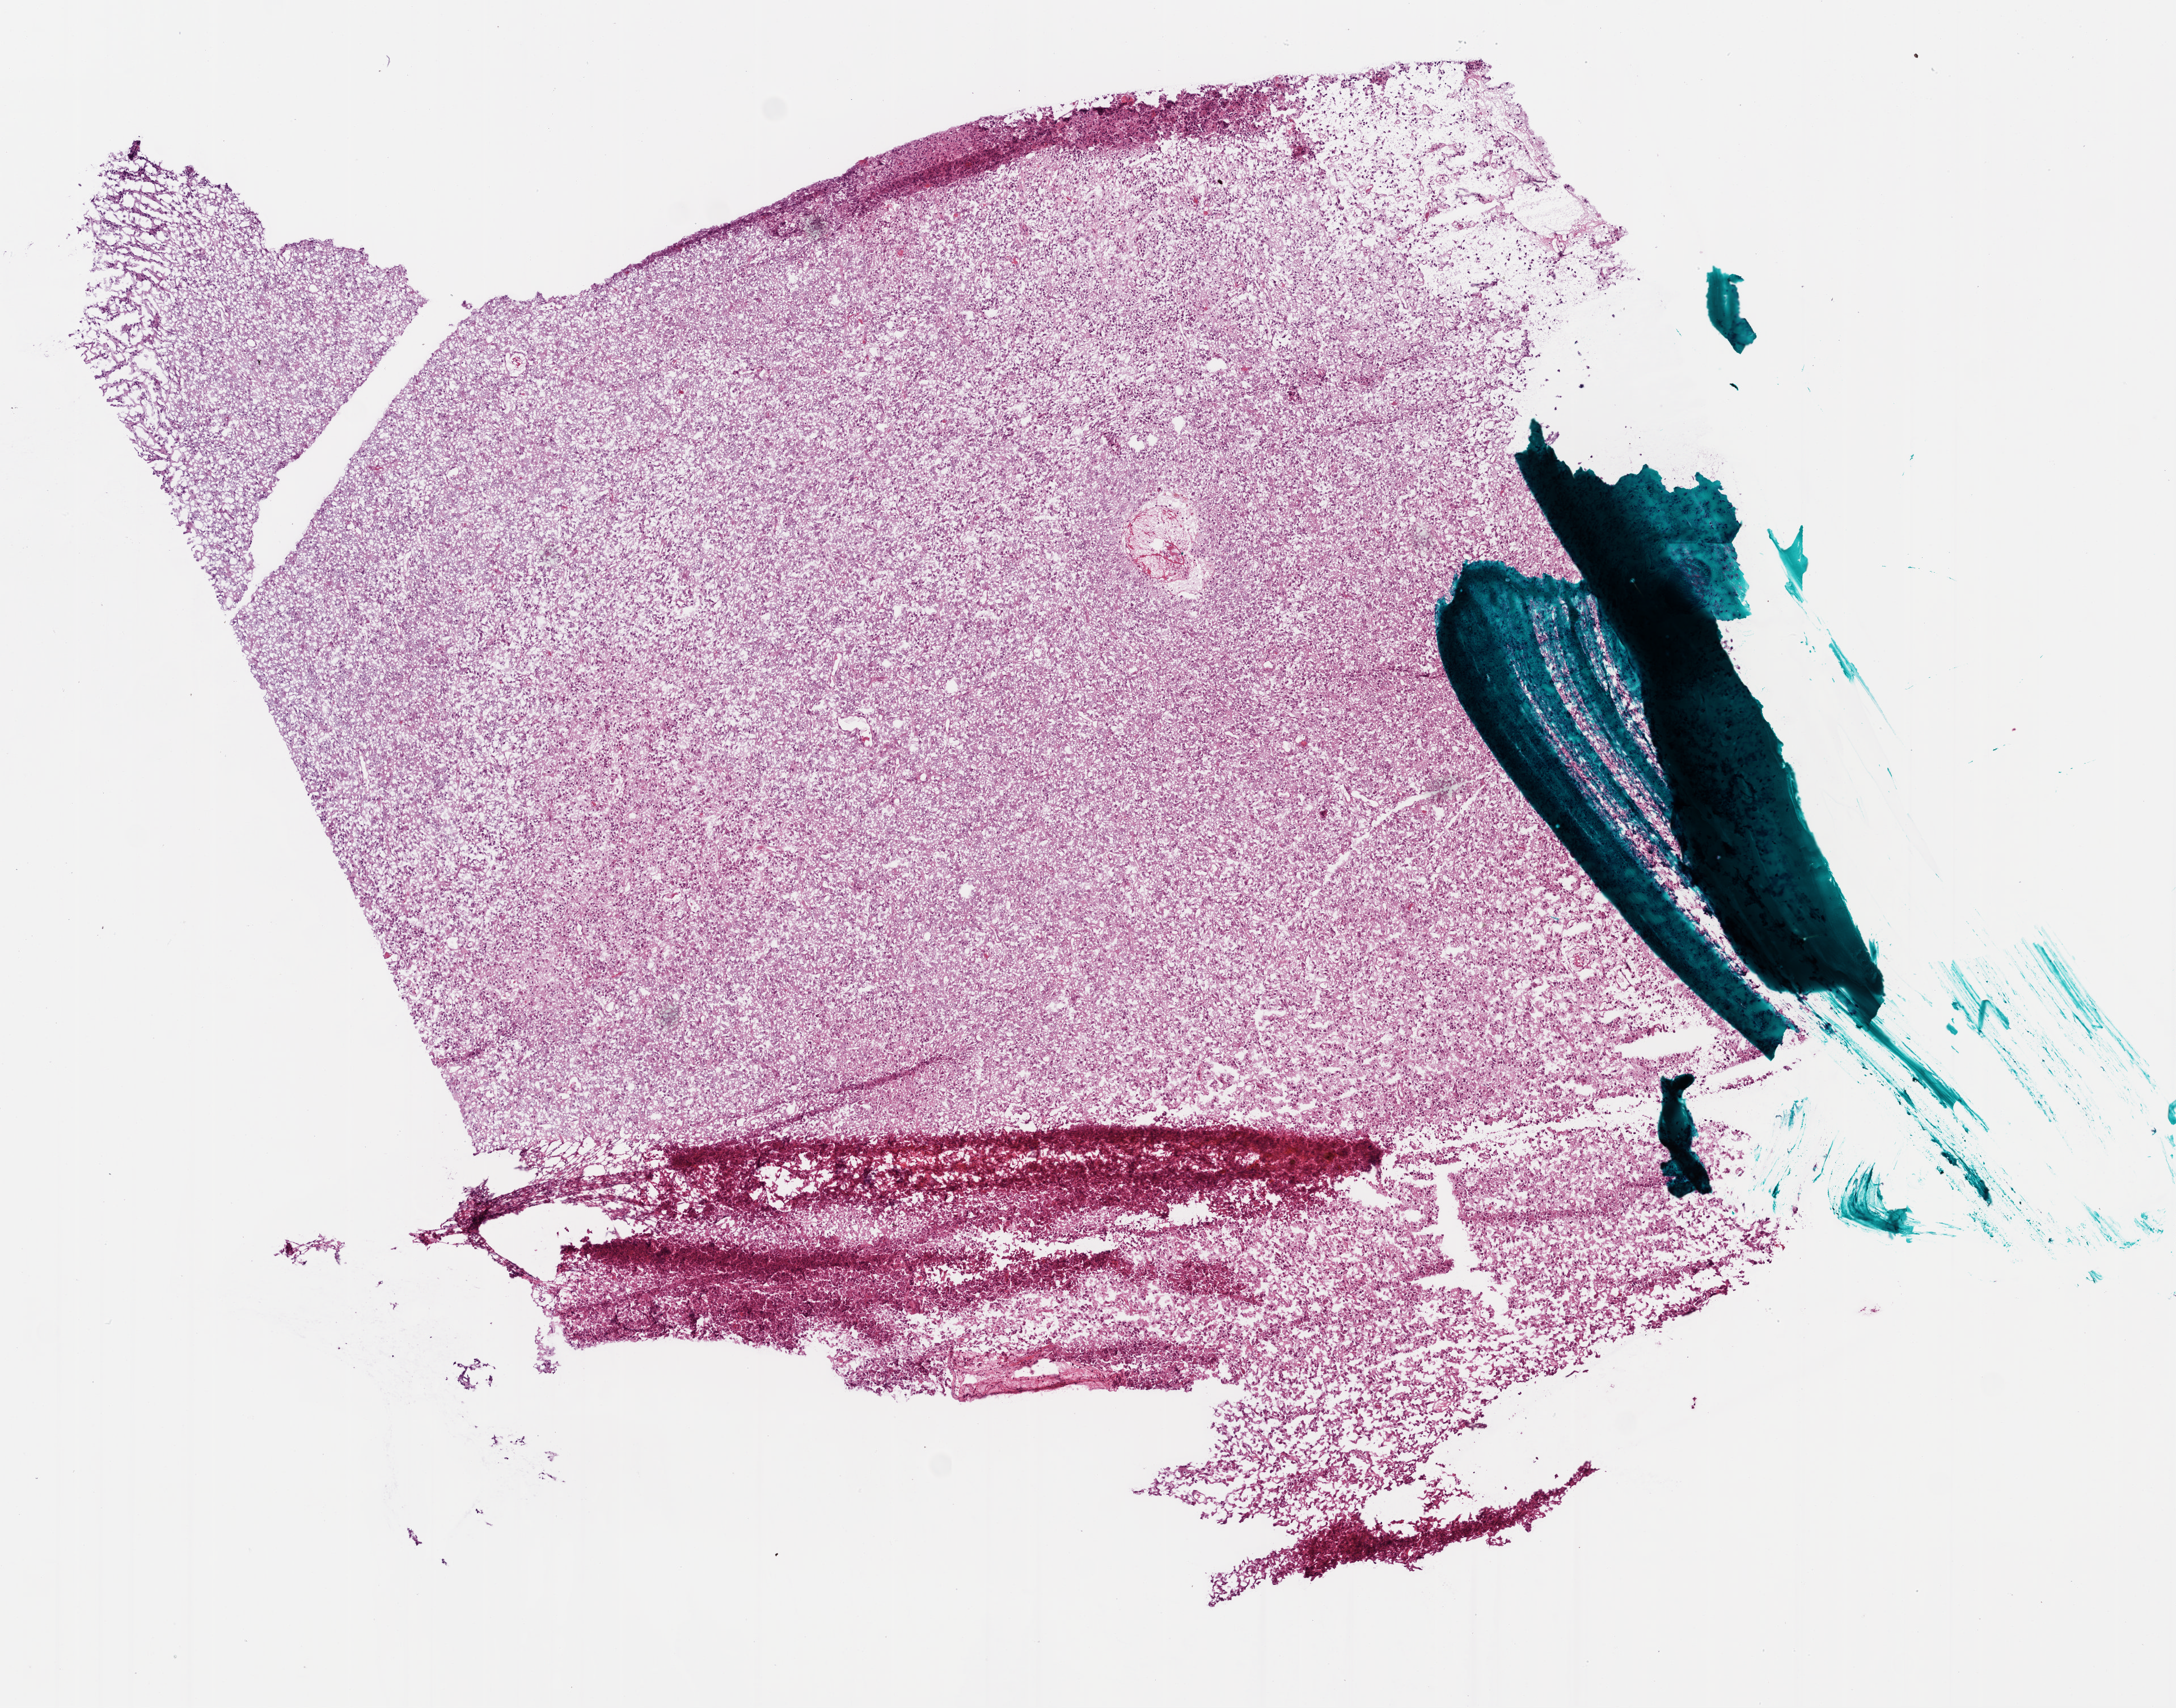
Hematoxylin and eosin (H&E) stained whole-slide image, shown as a low-resolution overview of the whole scanned area (about 7.7 x 6.1 mm); frozen section; brain, primary tumour sample. Male, age 46 years at initial diagnosis. Slide review estimates, as recorded: tumour cells 95%, tumour nuclei 95%, normal cells 0%, stromal cells 0%, necrosis 5%. Inflammatory infiltration, as recorded: monocyte infiltration 50%, neutrophil infiltration 50%.
Histologic diagnosis: Glioblastoma.